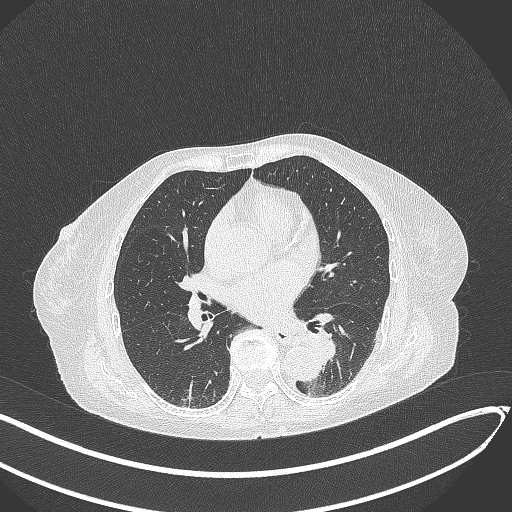
Chest CT, one axial slice. Position 121 of 324 along the scan axis. Reconstruction kernel B70f. 120 kVp. Lung window (W 1500 / L -600 HU). 1 mm slice thickness. 512 × 512 image matrix, field of view 400 × 400 mm. Female patient, age 82 years. From the clinical record (not read from this slice): clinical TNM (as recorded): T1b N0 M1.
Structures marked on this image (rectangle marked by the reading radiologist):
- lung tumour (recorded histology: adenocarcinoma): bounding box [x1, y1, x2, y2] px = [299, 326, 344, 368]